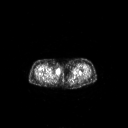
FDG PET of an extremity soft-tissue mass (from a PET/CT study), one axial slice. Slice 228 of 311 in the series (ordered by position). 128 × 128 image matrix, field of view 700 × 700 mm. Female patient, age 78 years. Case-level facts recorded for this patient, not image findings: histological type: leiomyosarcoma; grade: intermediate; site of the primary tumour: parascapusular.
Outlined on this slice (expert contour drawn on MRI and transferred to this co-registered scan by the dataset authors):
- gross tumour volume including surrounding oedema: bounding box <55,69,61,75> (left, top, right, bottom; pixels)
- gross tumour volume (mass): <55,70,61,74>